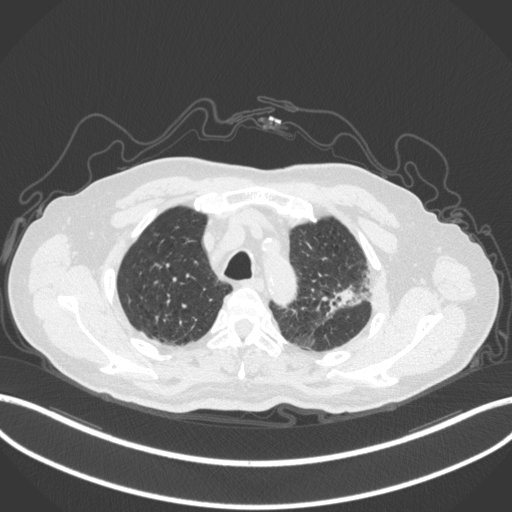
Chest CT, one axial slice. Slice 243 of 331 in the series (ordered by position). Reconstruction kernel B31f. 120 kVp. Lung window (W 1500 / L -600 HU). 512 × 512 image matrix, field of view 400 × 400 mm. Male patient, age 79 years. Case-level facts recorded for this patient, not image findings: clinical TNM (as recorded): T2a N1 M1; histopathological grade: G3.
Structures marked on this image (bounding box drawn by a radiologist):
- lung tumour (recorded histology: adenocarcinoma): bounding box <326,276,373,322> (left, top, right, bottom; pixels)